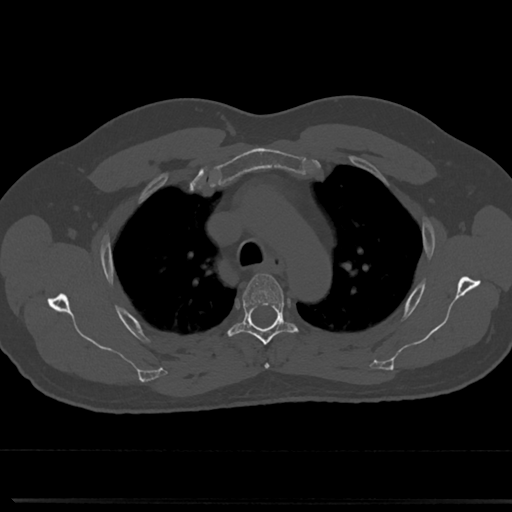
CT including the spine, one axial slice. Position 550 of 817 along the scan axis. 120 kVp. Bone window (W 1800 / L 400 HU). 512 × 512 image matrix. Male patient, age 61 years. Case-level facts recorded for this patient, not image findings: primary cancer: prostate.
Outlined on this slice (semi-automatic segmentation, software-assisted and operator-edited):
- T3 vertebra: bounding box <264,363,269,368> (left, top, right, bottom; pixels)
- T4 vertebra: <223,273,300,345>